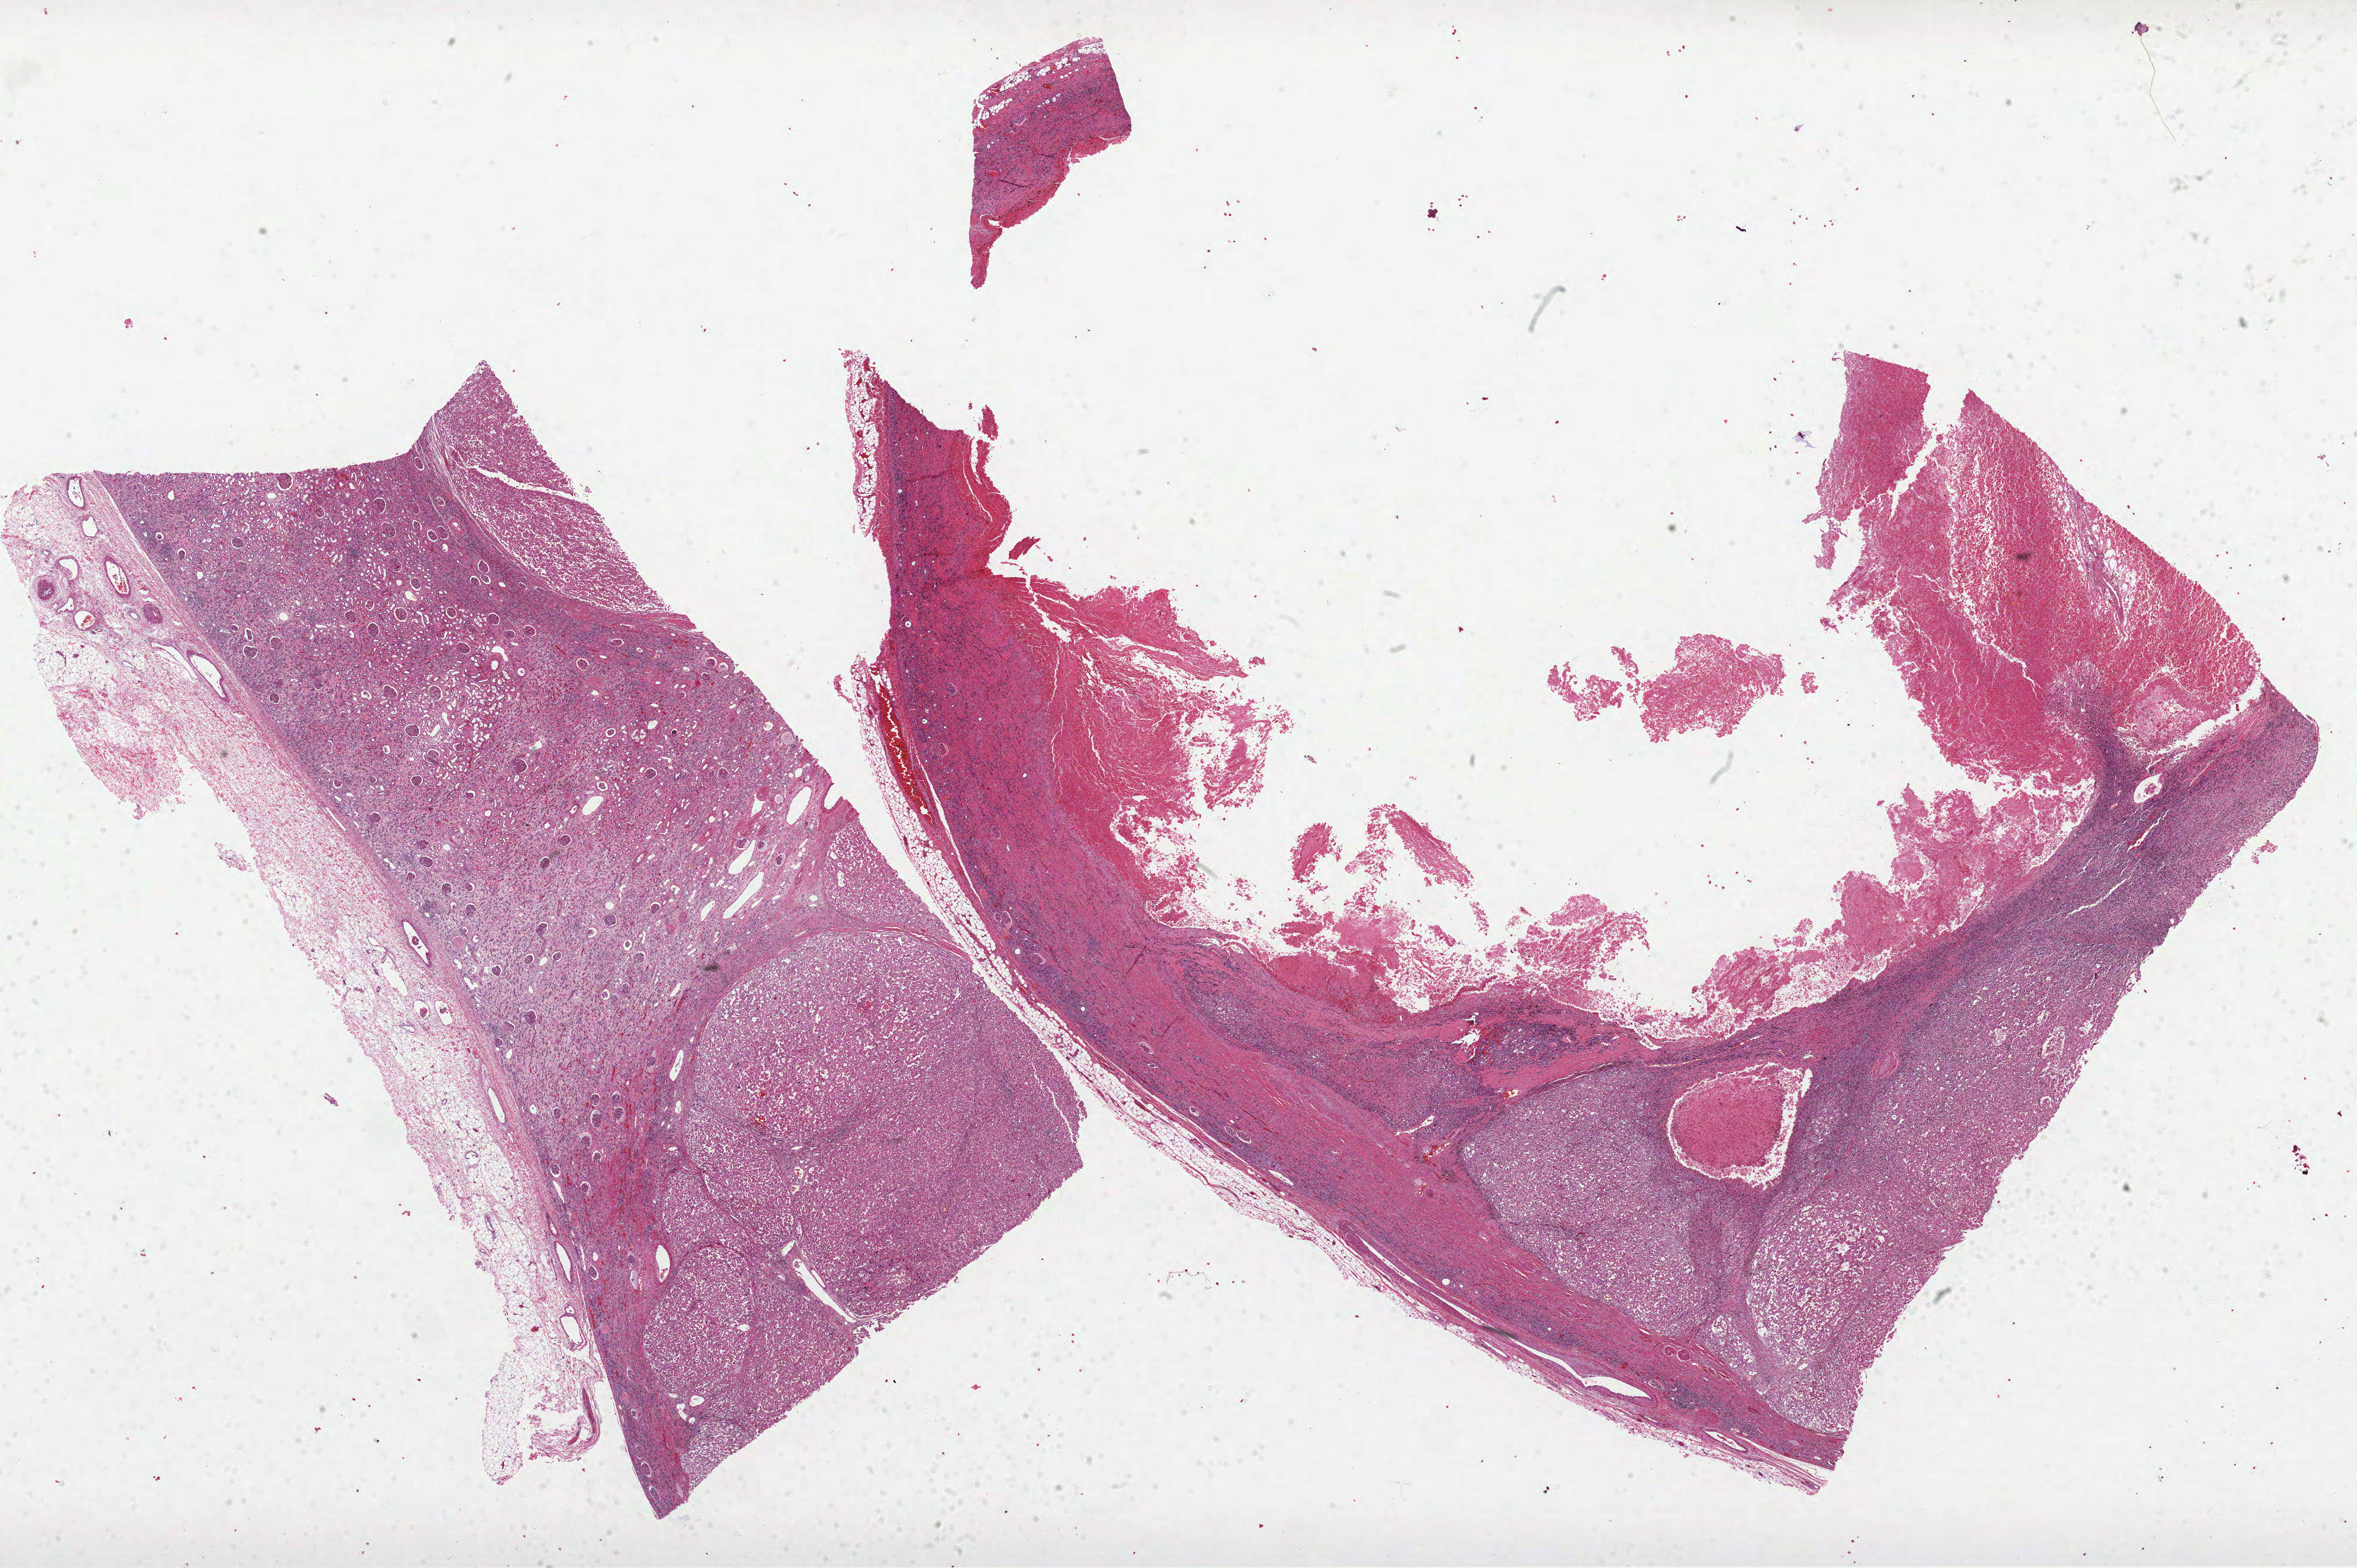
H&E whole-slide image — a low-resolution overview of the entire scanned area, about 32.1 x 21.4 mm, formalin-fixed paraffin-embedded (FFPE) diagnostic section, kidney, primary tumour sample. Patient: male, age at initial diagnosis 46 years. Histologic grade: G4 (undifferentiated).
AJCC pathologic stage: IV. Laterality: left. TNM: T4 N0 M1. Diagnosis: Clear cell adenocarcinoma, NOS.